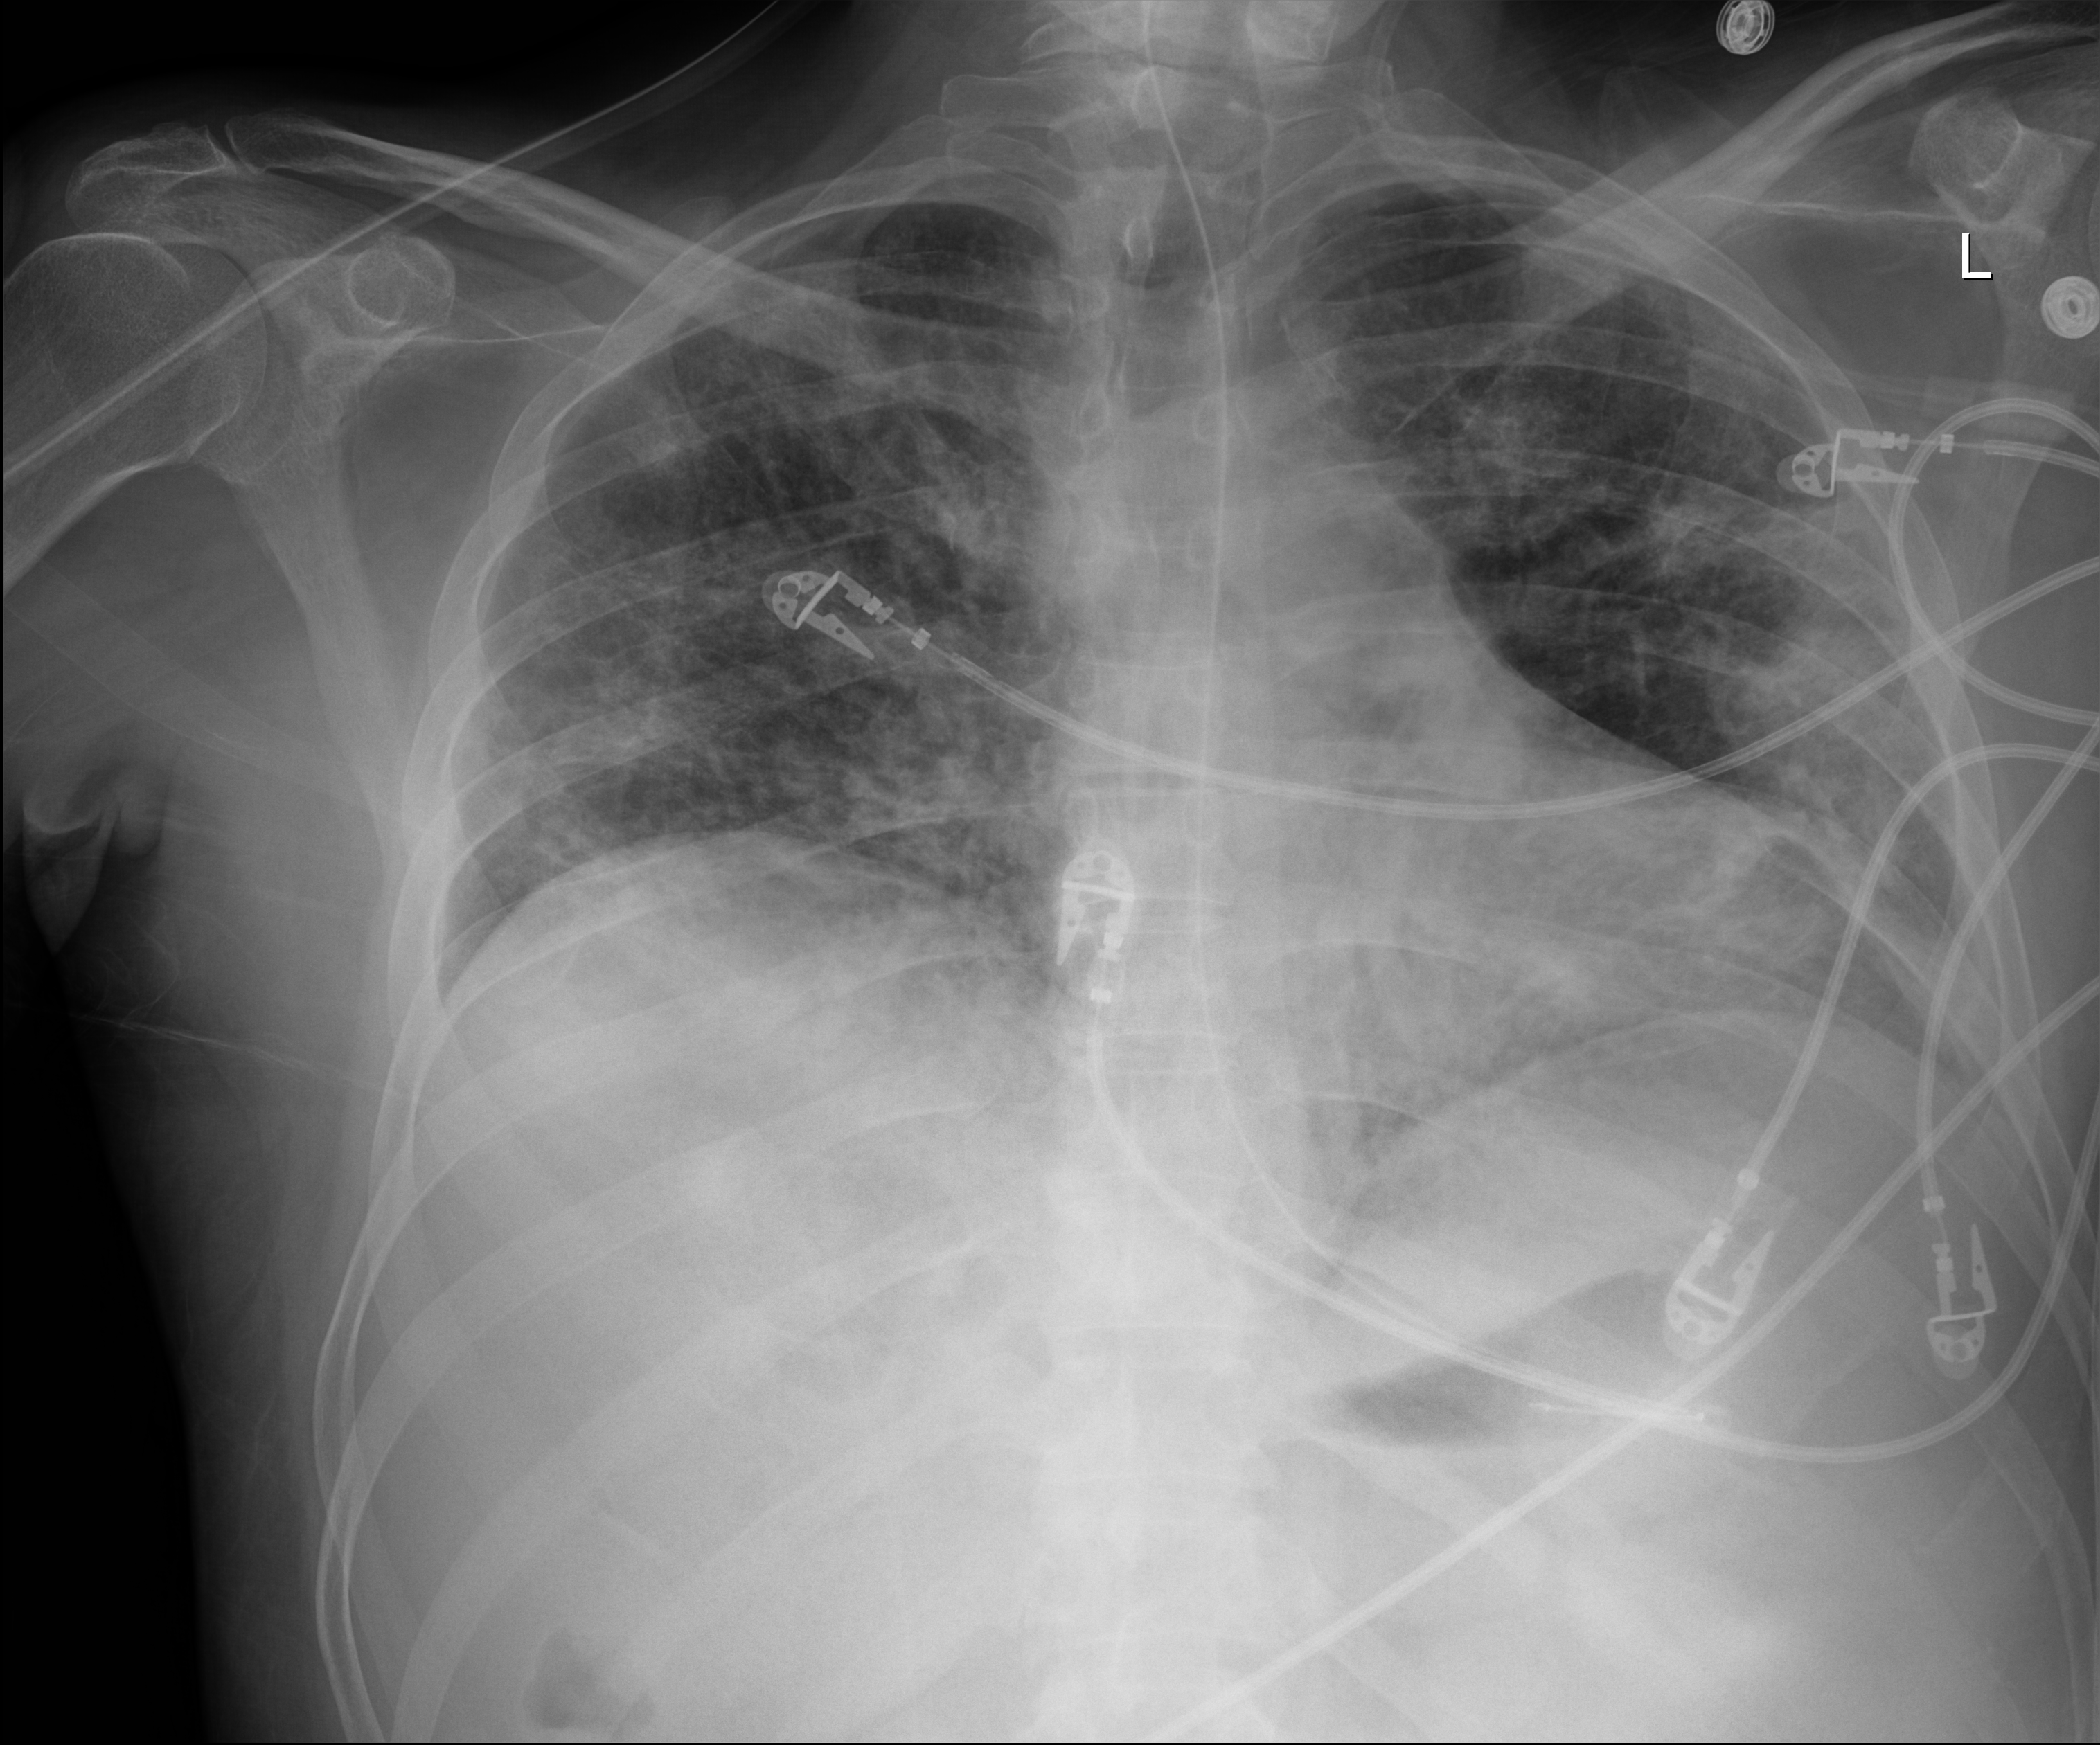
Portable chest radiograph; anteroposterior (AP) projection. Patient hospitalised with COVID-19; male, aged 18–59 years.
From the hospital-stay record, not from the radiograph (when in the stay this image was taken is not recorded): admitted to intensive care during this hospital stay: yes; mechanically ventilated during this hospital stay: yes.